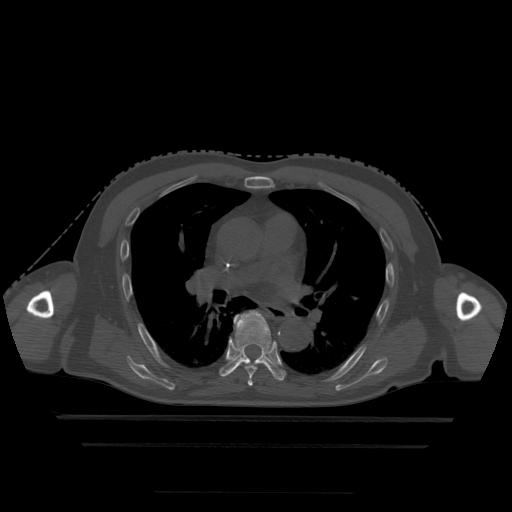
CT including the spine, one axial slice. Slice 307 of 522 in the series (ordered by position). Bone window (W 1800 / L 400 HU). 1.25 mm slice thickness. 512 × 512 image matrix, field of view 436 × 436 mm. Patient age 68 years. Case-level facts recorded for this patient, not image findings: primary cancer: urothelial.
Structures marked on this image (semi-automatically segmented with operator editing):
- T5 vertebra: bounding box [x1, y1, x2, y2] px = [248, 378, 254, 387]
- T6 vertebra: [246, 365, 257, 379]
- T7 vertebra: [220, 311, 286, 381]